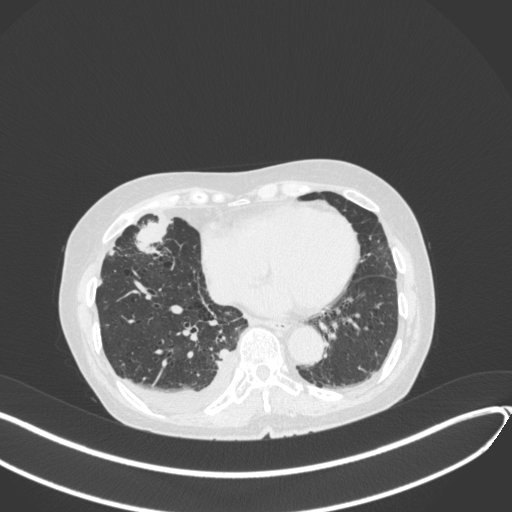
Chest CT, one axial slice. Lung window (W 1500 / L -600 HU). 512 × 512 image matrix. Female patient, age 75 years. From the clinical record (not read from this slice): clinical TNM (as recorded): T2a N3 M0.
Structures marked on this image (rectangle marked by the reading radiologist):
- lung tumour (recorded histology: adenocarcinoma): bounding box <132,208,173,257> (left, top, right, bottom; pixels)